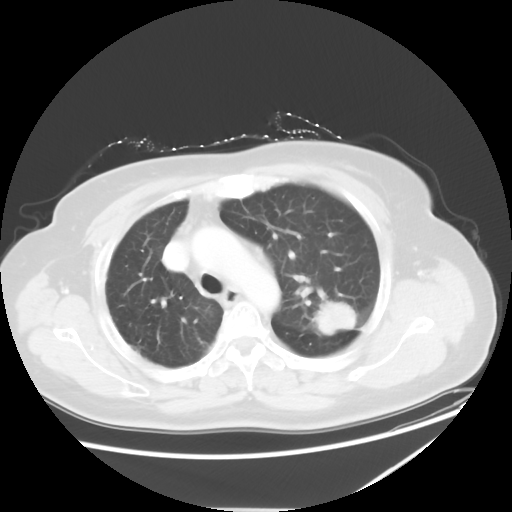
Chest CT, one axial slice. Reconstruction kernel STANDARD. 120 kVp. Lung window (W 1500 / L -600 HU). 5 mm slice thickness. 512 × 512 image matrix, field of view 384 × 384 mm. Female patient, age 61 years. Case-level facts recorded for this patient, not image findings: clinical TNM (as recorded): T1c N3 M1.
Outlined on this slice (rectangle marked by the reading radiologist):
- lung tumour (recorded histology: adenocarcinoma): box from (x=313, y=296) to (x=361, y=337) px